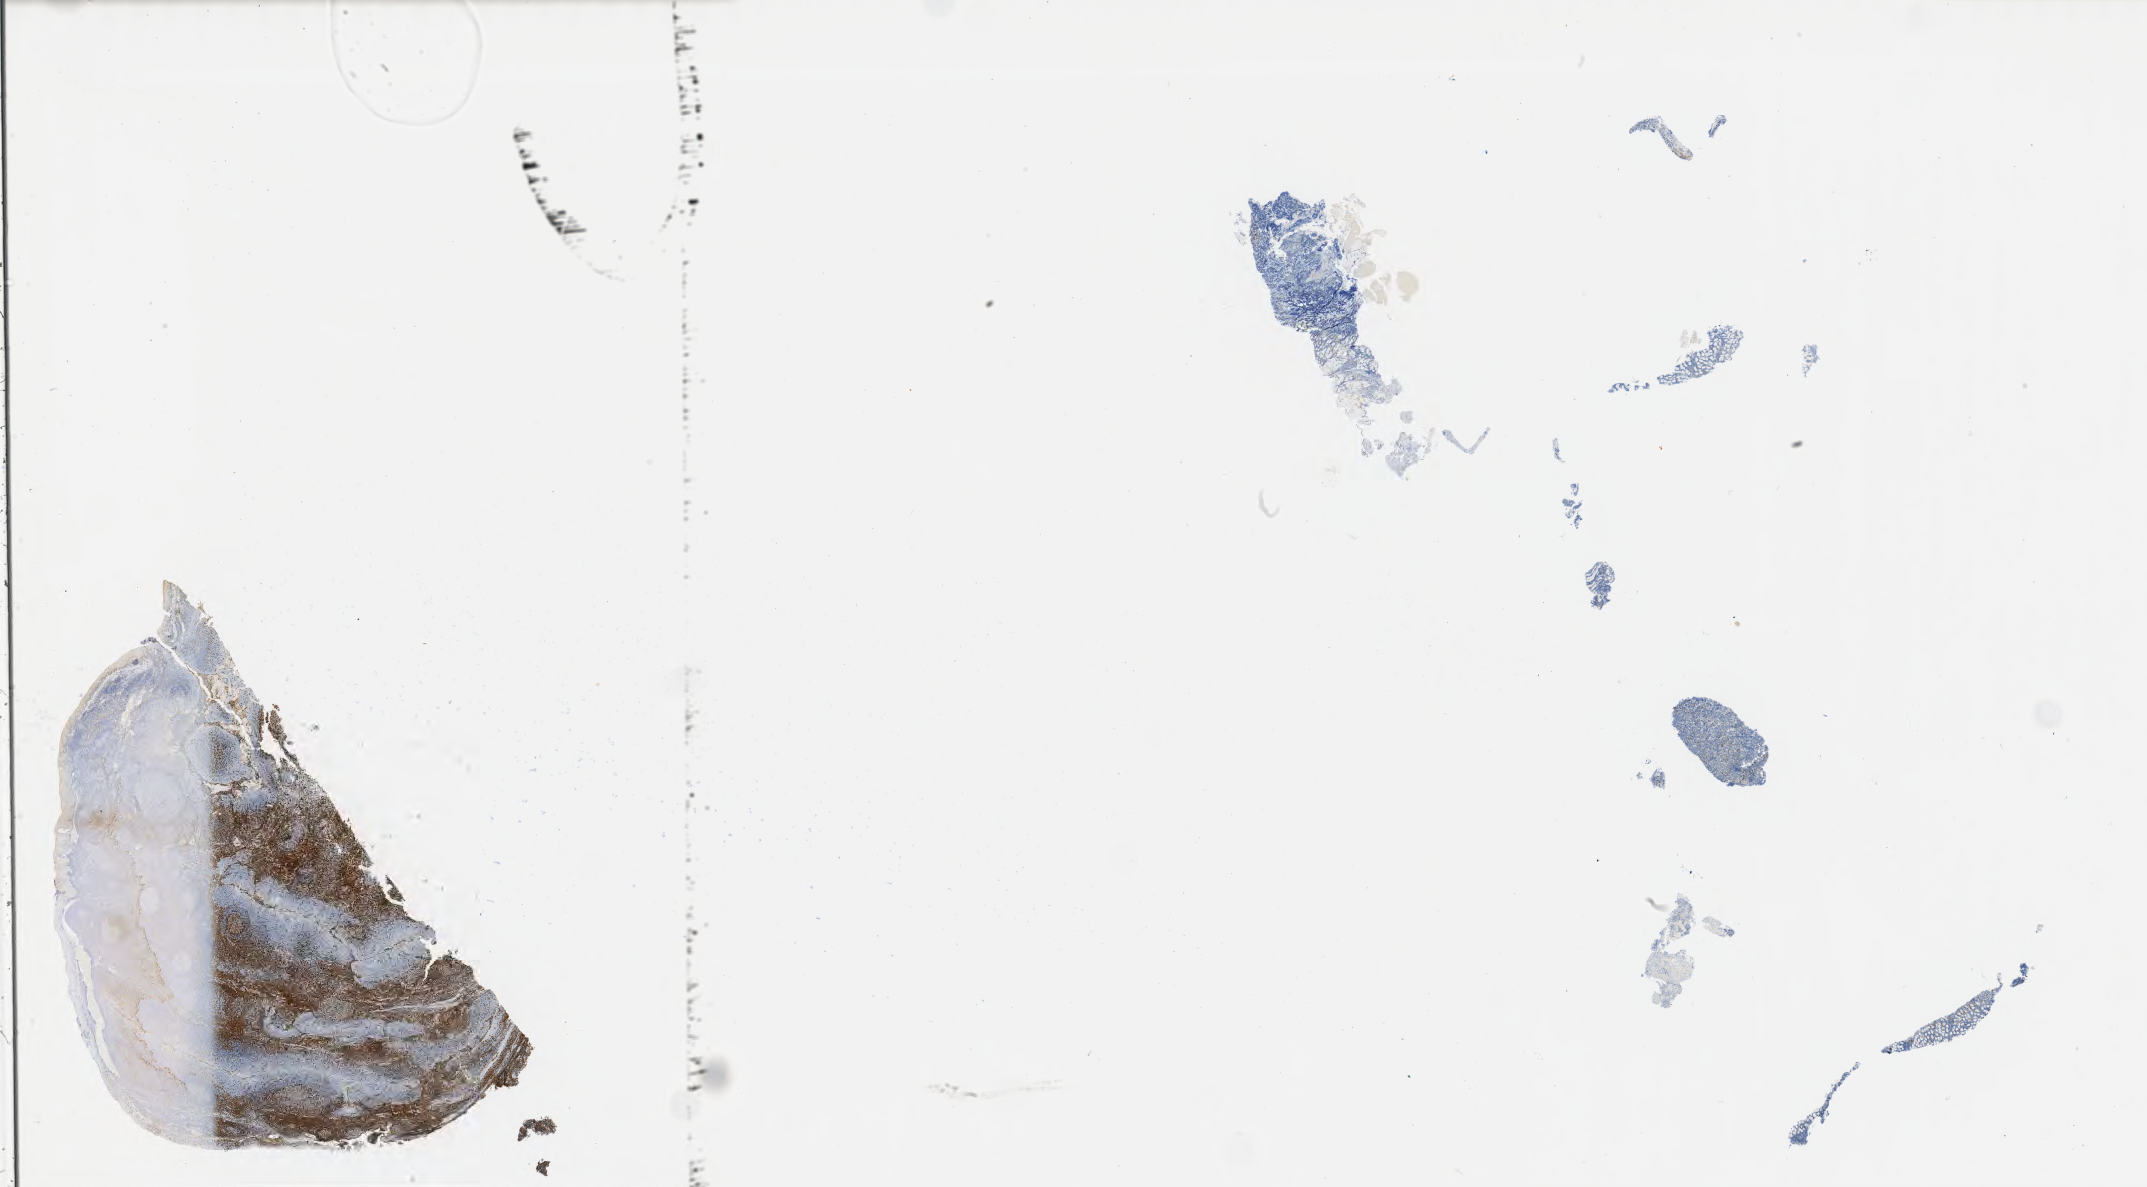
Immunohistochemistry (IHC) whole-slide image stained for CD3, whole scanned area (about 34.7 x 19.2 mm) shown as a low-resolution overview; specimen: tumor tissue; site: bone of pelvis. Male patient, age 53 years.
Diagnosis: Burkitt lymphoma, NOS.